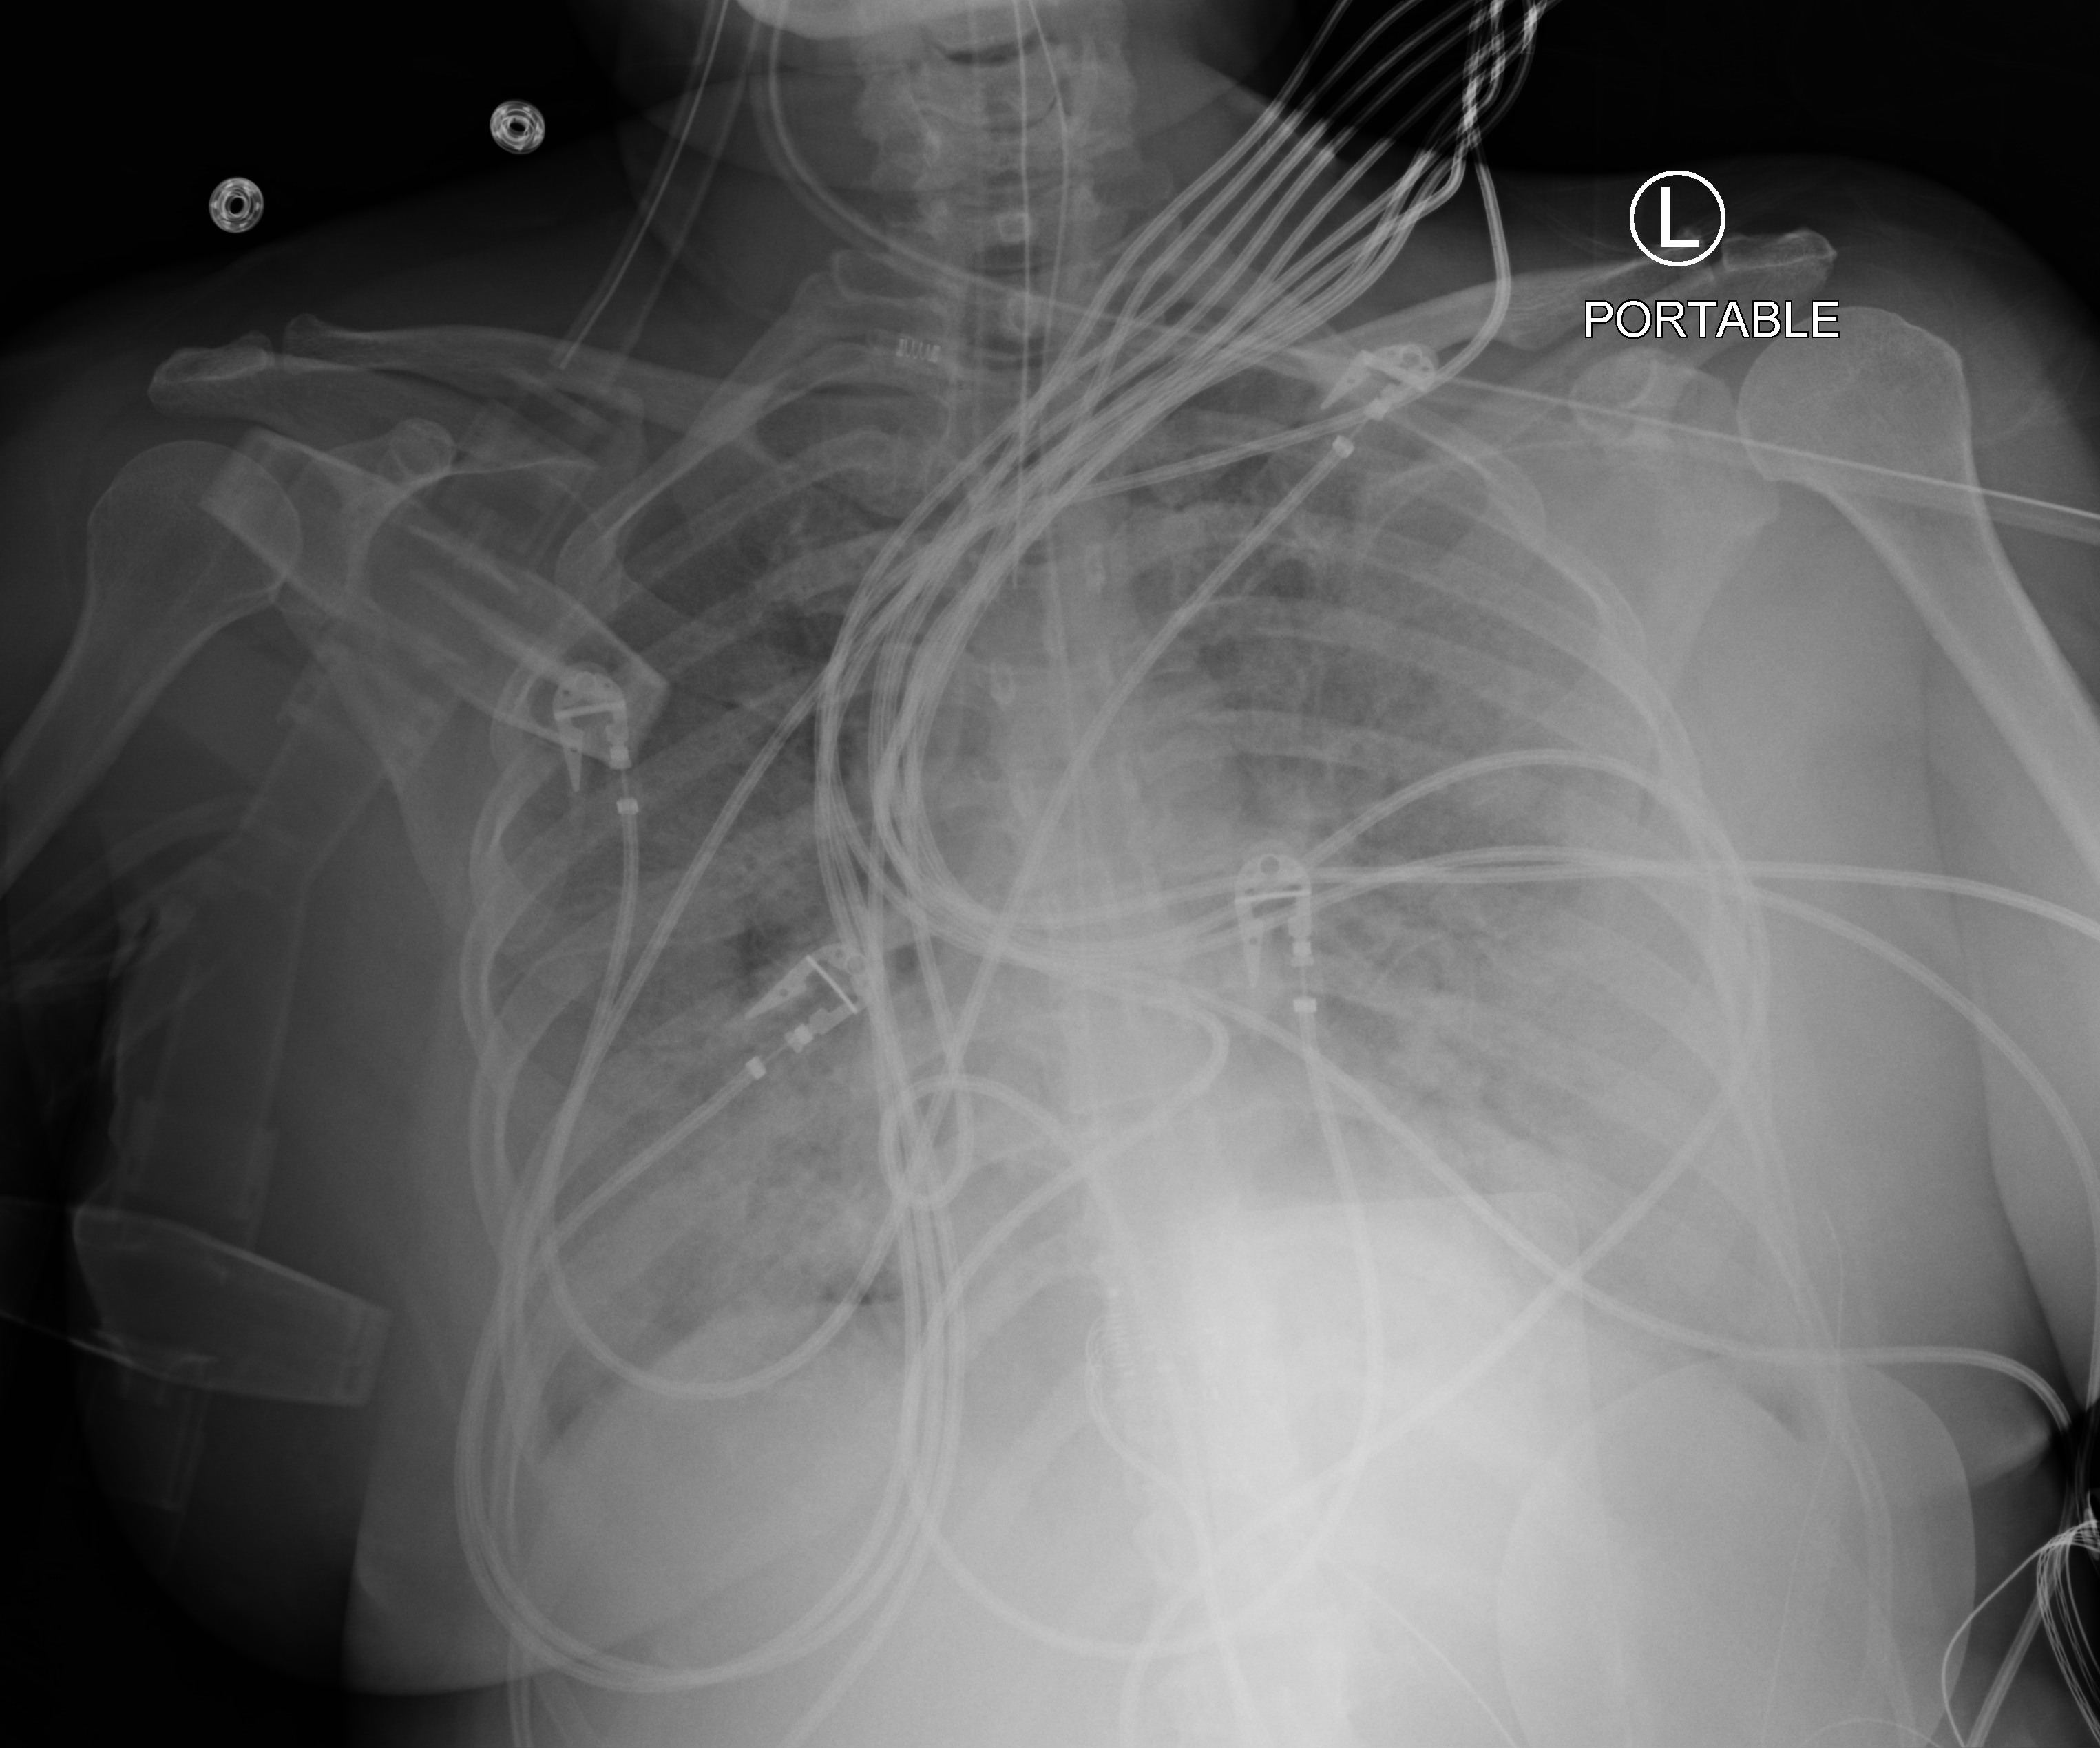
Chest X-ray (portable); anteroposterior (AP) projection. Patient hospitalised with COVID-19; male, aged 18–59 years.
Admission-level facts for this patient (not findings on this image; timing relative to this image not recorded): admitted to intensive care during this hospital stay: yes.